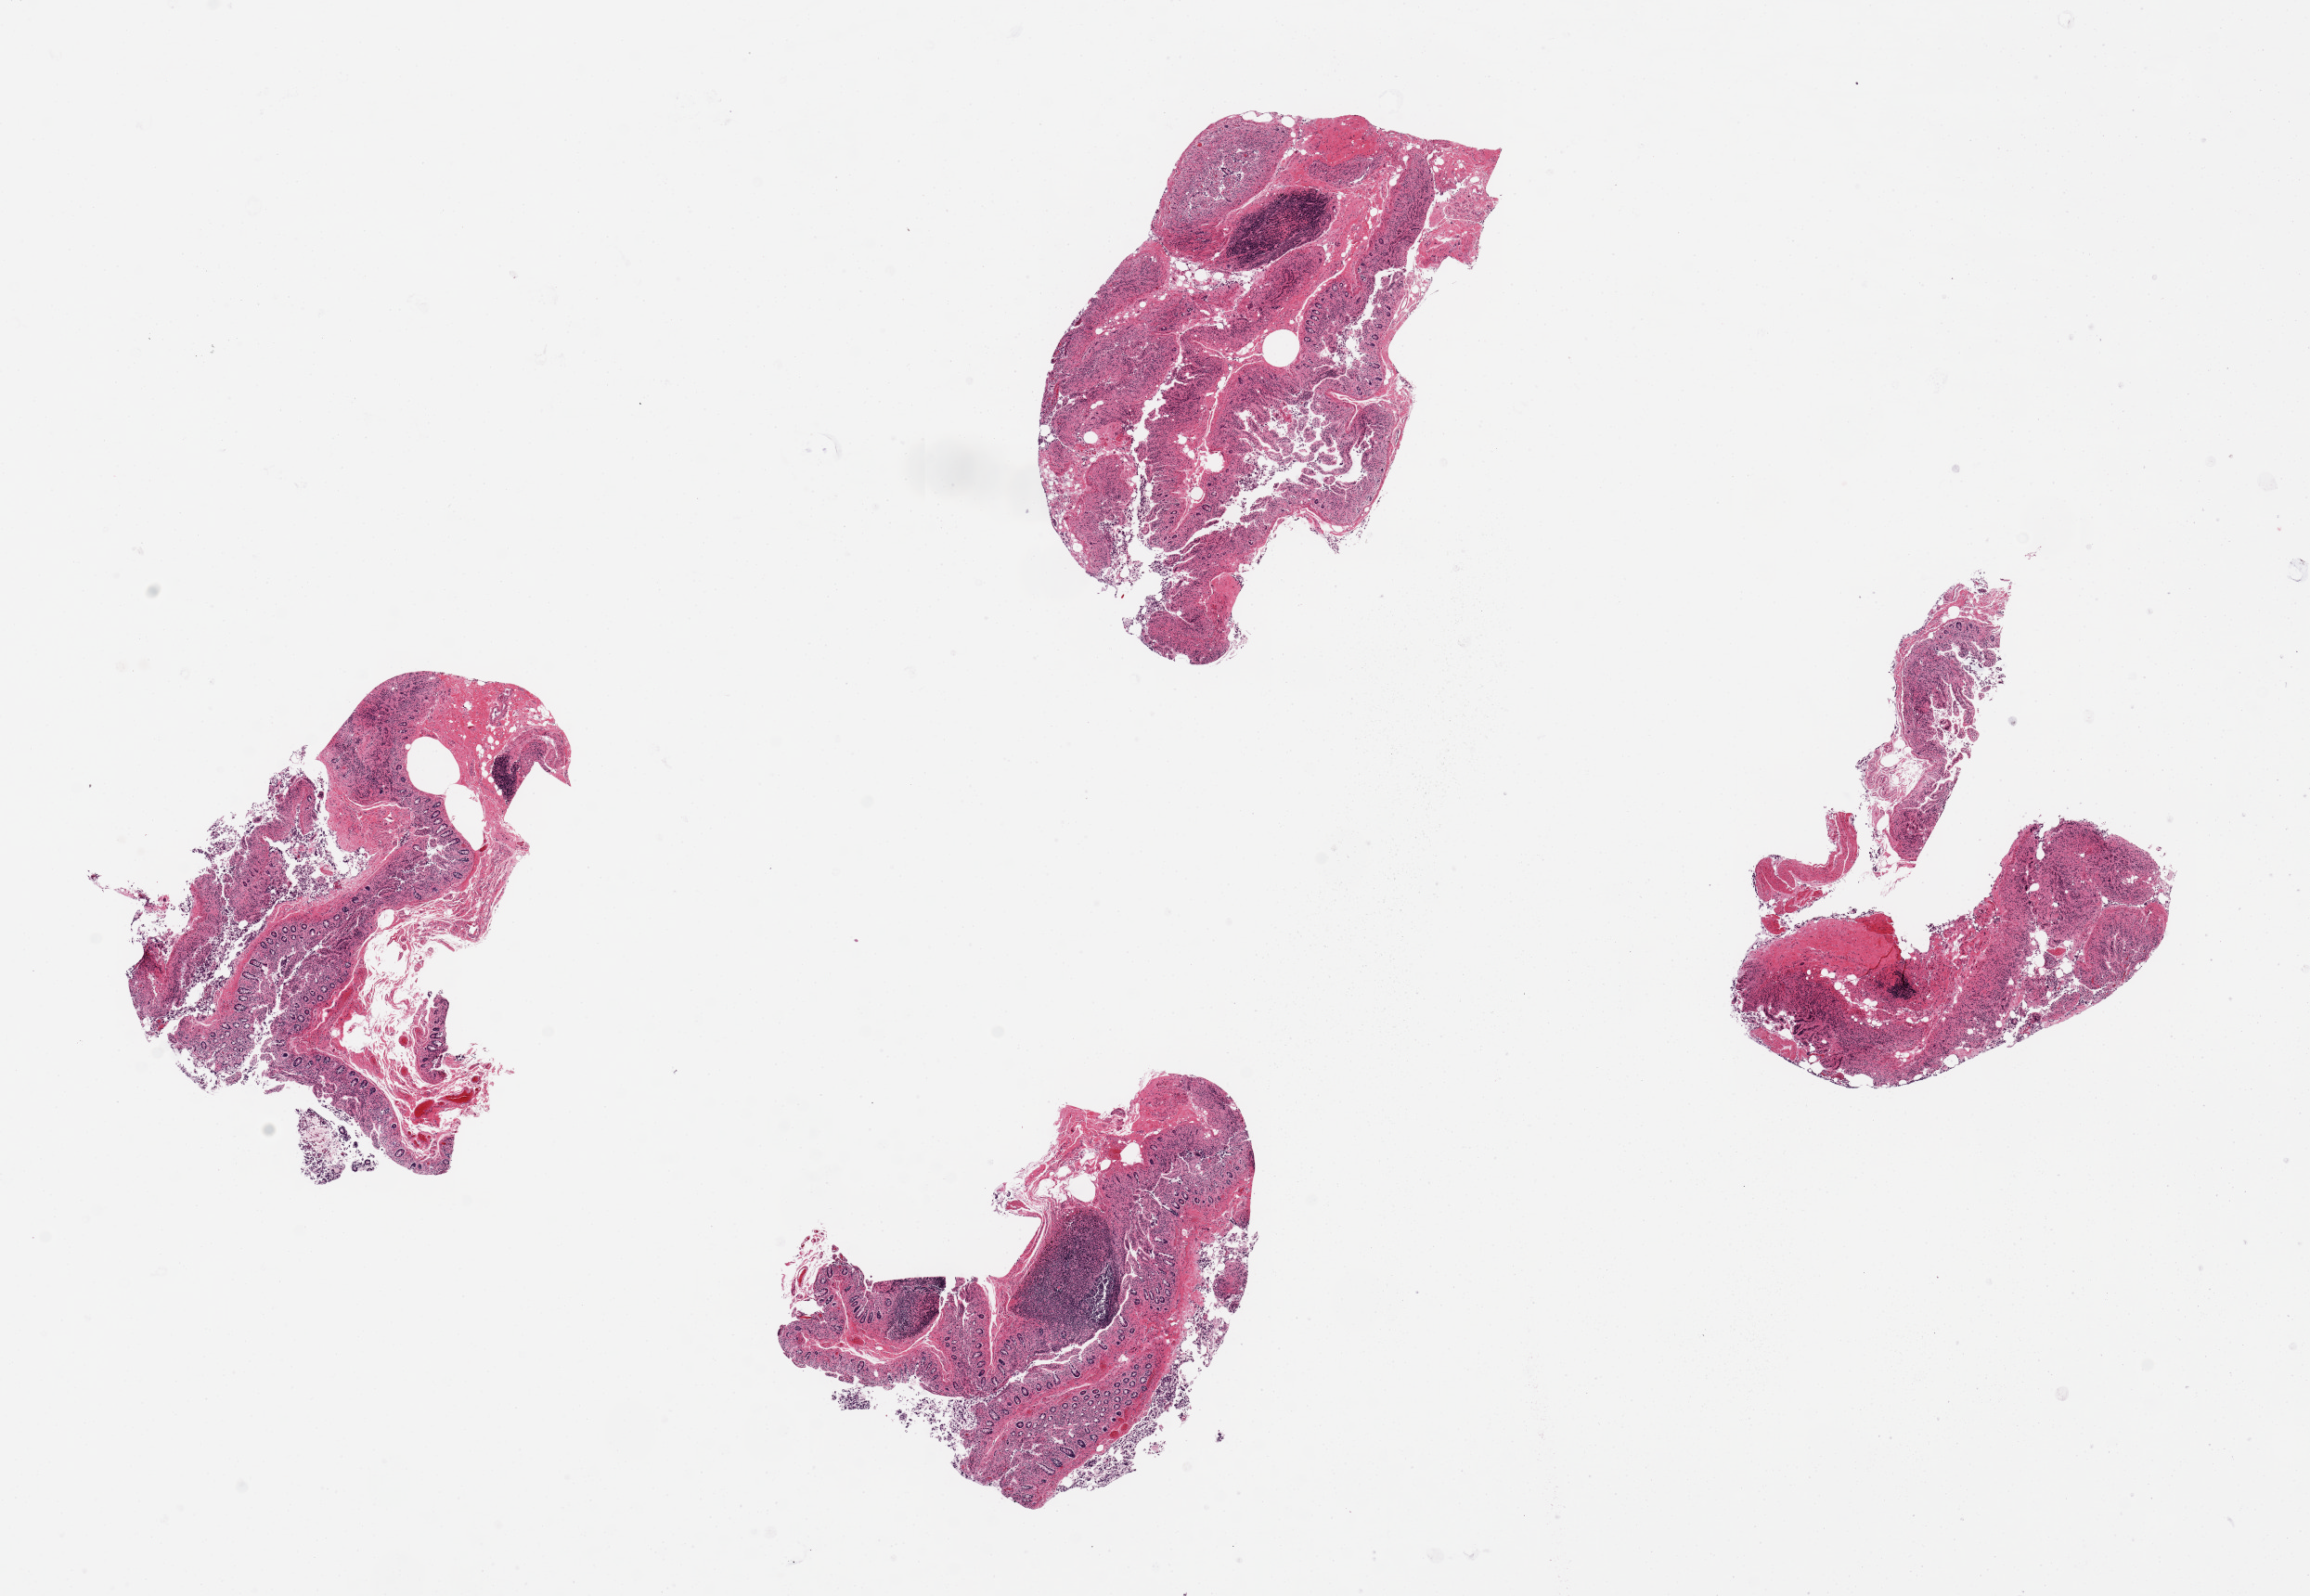
Whole-slide image, haematoxylin and eosin stain — a low-resolution overview of the entire scanned area, about 19.7 x 13.6 mm, PAXgene-fixed paraffin-embedded (PFPE) section, sampled site (target tissue): ileum, donor tissue sample. Male donor.
Review note (as recorded): 4 pieces; up to 5x3mm; ~5% lymphoid elements.